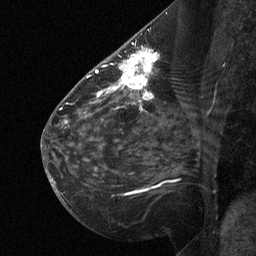
Breast MRI (dynamic contrast-enhanced), one sagittal slice. Position 35 of 64 along the scan axis. Dynamic contrast-enhanced study with each time point stored as its own series, time point 2 of 3 at this slice position (early post-contrast, ordered by acquisition time). 1.5 T. TE 4.8 ms, TR 27 ms. 256 × 256 image matrix. Patient: female, 51 years. From the clinical record (not read from this slice): setting: breast cancer imaged before/during neoadjuvant chemotherapy; receptor status: HR-positive, HER2-negative.
Outlined on this slice (semi-automatic segmentation, software-assisted and operator-edited):
- analysis volume of interest (the breast-tissue region the enhancement analysis was run in; not a lesion): bounding box [x1, y1, x2, y2] px = [112, 46, 162, 106]
- tumour enhancement mask (voxels above the 90 % enhancement threshold inside the analysis volume of interest): [112, 49, 157, 102]